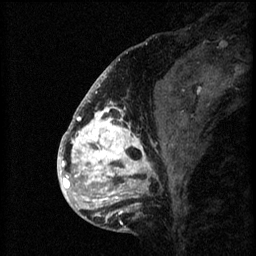
Breast MRI (dynamic contrast-enhanced), one sagittal slice; slice 25 of 60 in the series (ordered by position); 3 images stored at this slice position (order not interpretable as contrast timing); 1.5 T; TE 4.2 ms, TR 8.2 ms; 256 × 256 image matrix, field of view 180 × 180 mm. Patient: female, 41 years.
Outlined on this slice (semi-automatically segmented with operator editing):
- analysis volume of interest (the breast-tissue region the enhancement analysis was run in; not a lesion): box from (x=72, y=108) to (x=176, y=205) px
- tumour enhancement mask (voxels above the 70 % enhancement threshold inside the analysis volume of interest): (x=72, y=108)–(x=153, y=205)